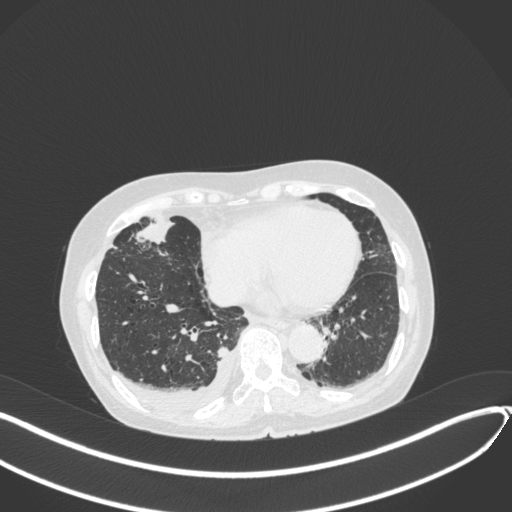
Chest CT, one axial slice. Position 124 of 418 along the scan axis. Reconstruction kernel B31f. 120 kVp. Lung window (W 1500 / L -600 HU). 512 × 512 image matrix, field of view 400 × 400 mm. Female patient, age 75 years. Case-level facts recorded for this patient, not image findings: clinical TNM (as recorded): T2a N3 M0.
Annotated regions visible in this slice (rectangle marked by the reading radiologist):
- lung tumour (recorded histology: adenocarcinoma): box from (x=133, y=217) to (x=173, y=246) px